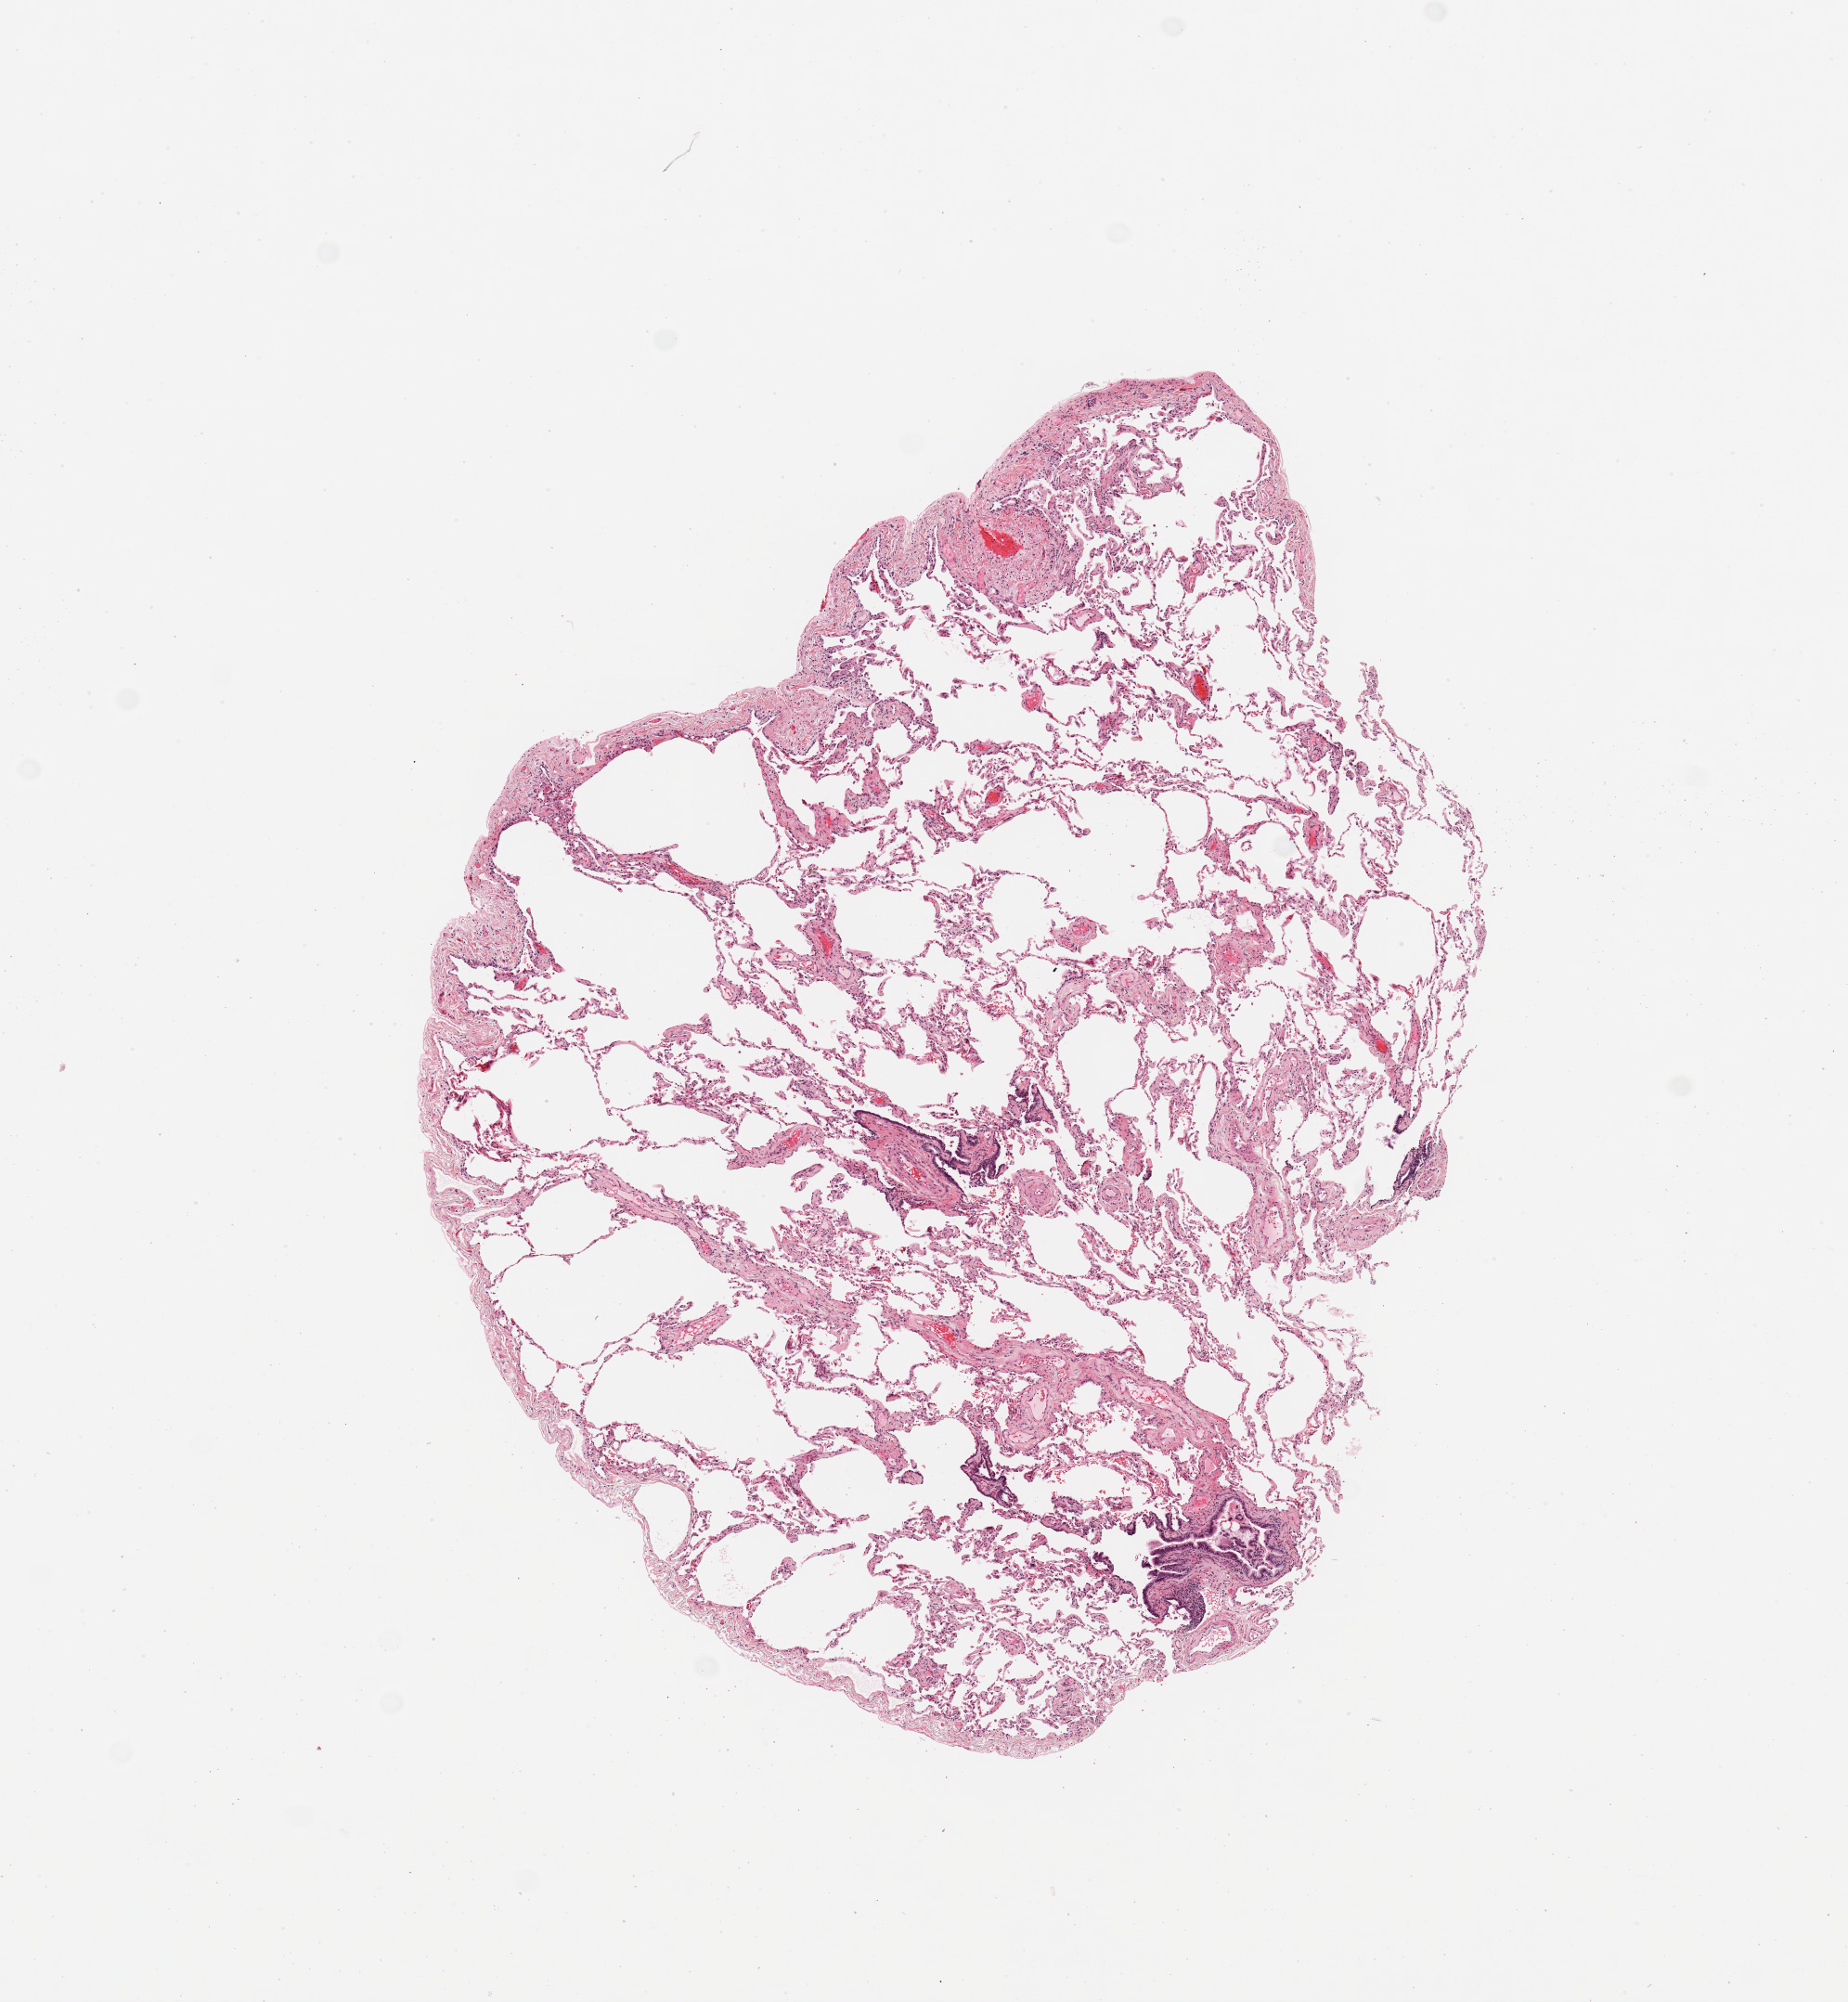
Hematoxylin and eosin (H&E) stained whole-slide image — a low-resolution overview of the entire scanned area, about 7.9 x 8.5 mm (from a 20x scan). Normal (non-tumour) tissue sample, sampled site: lung. Patient: female, age 70 years.
This section: normal (non-tumour) tissue from the same patient. Patient diagnosis: Adenocarcinoma, NOS.